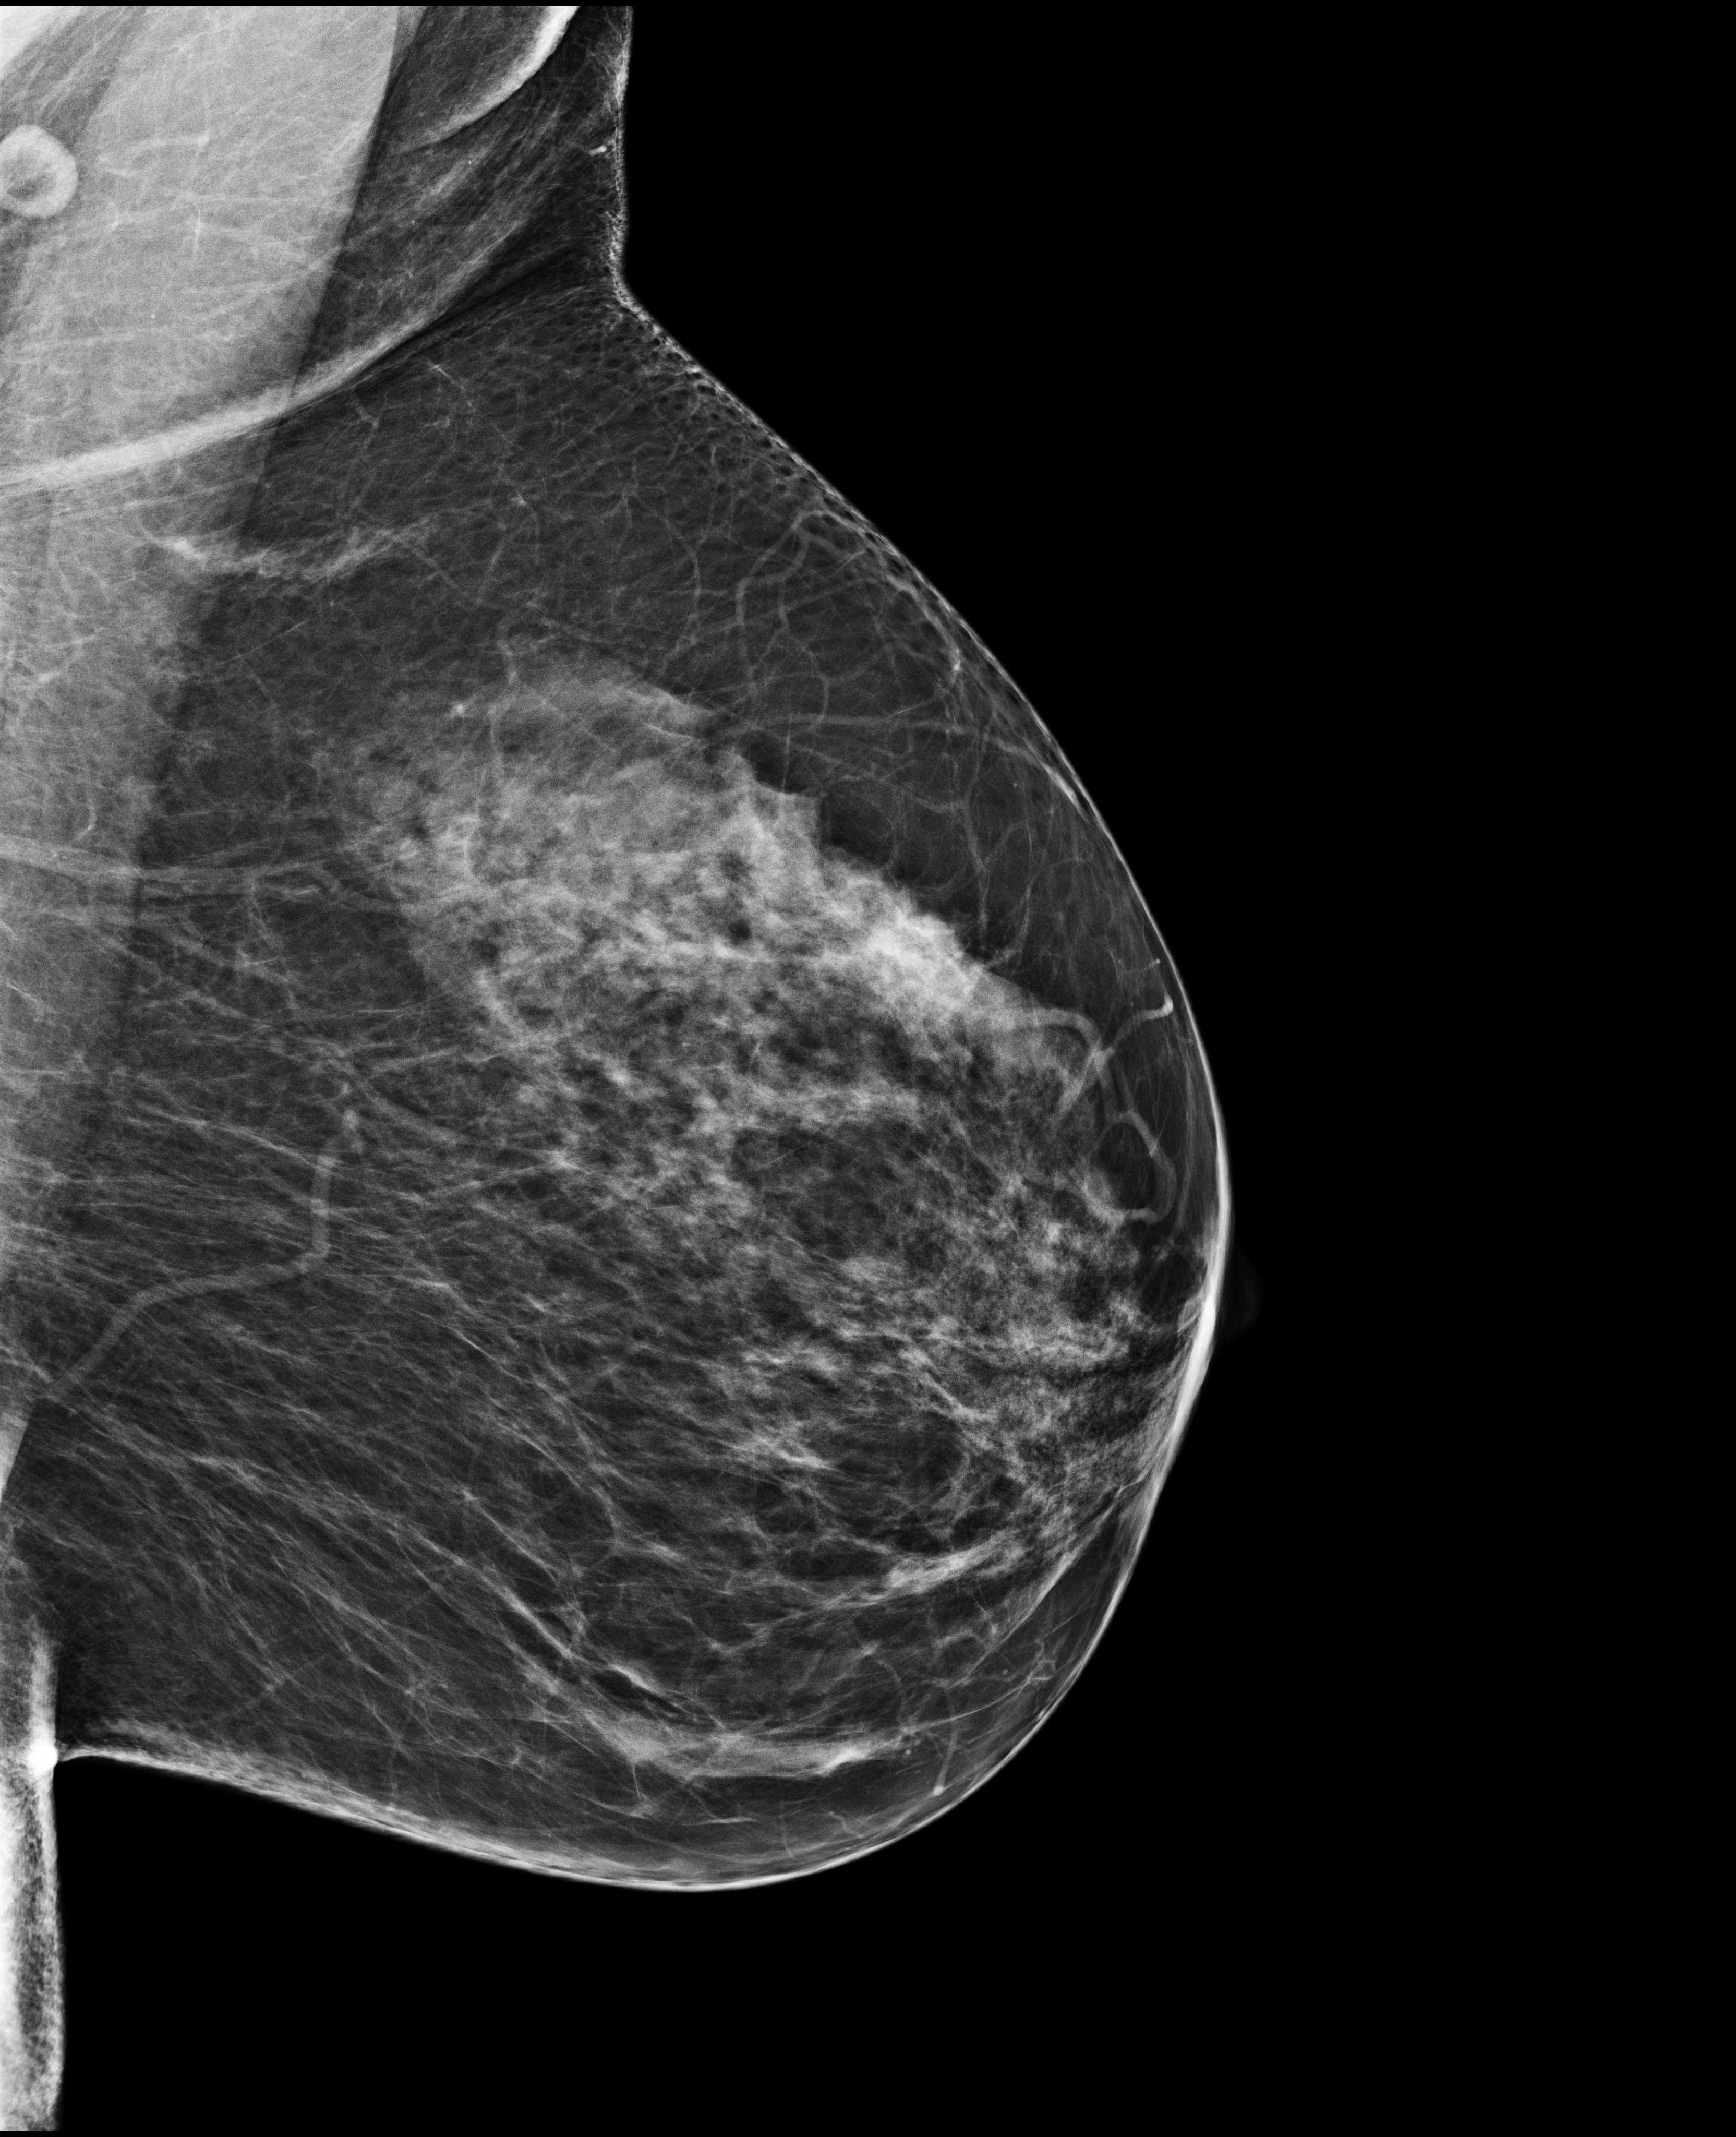
Full-field digital mammogram (FFDM); left breast; medio-lateral oblique projection; annual screening mammography examination. Patient aged 58 years (female).
BI-RADS breast density category at the screening exam (both breasts, scale 1–4): 3. Final BI-RADS assessment for this screening round (tomosynthesis exam, both breasts): category 1. Recall: no recall after this screen.